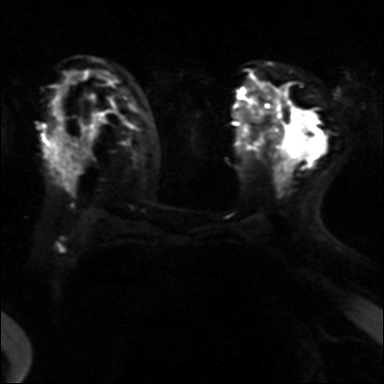
Breast MRI, one axial slice. Slice 21 of 40 in the series (ordered by position). Diffusion-weighted series; image 2 of 4 stored at this slice position (different b-values; order by instance number). 3 T. 384 × 384 image matrix. Female patient.
Annotated regions visible in this slice (outlined manually by an expert reader):
- tumour on diffusion-weighted imaging: bounding box (x1, y1, x2, y2) in pixels: (293, 110, 325, 157)